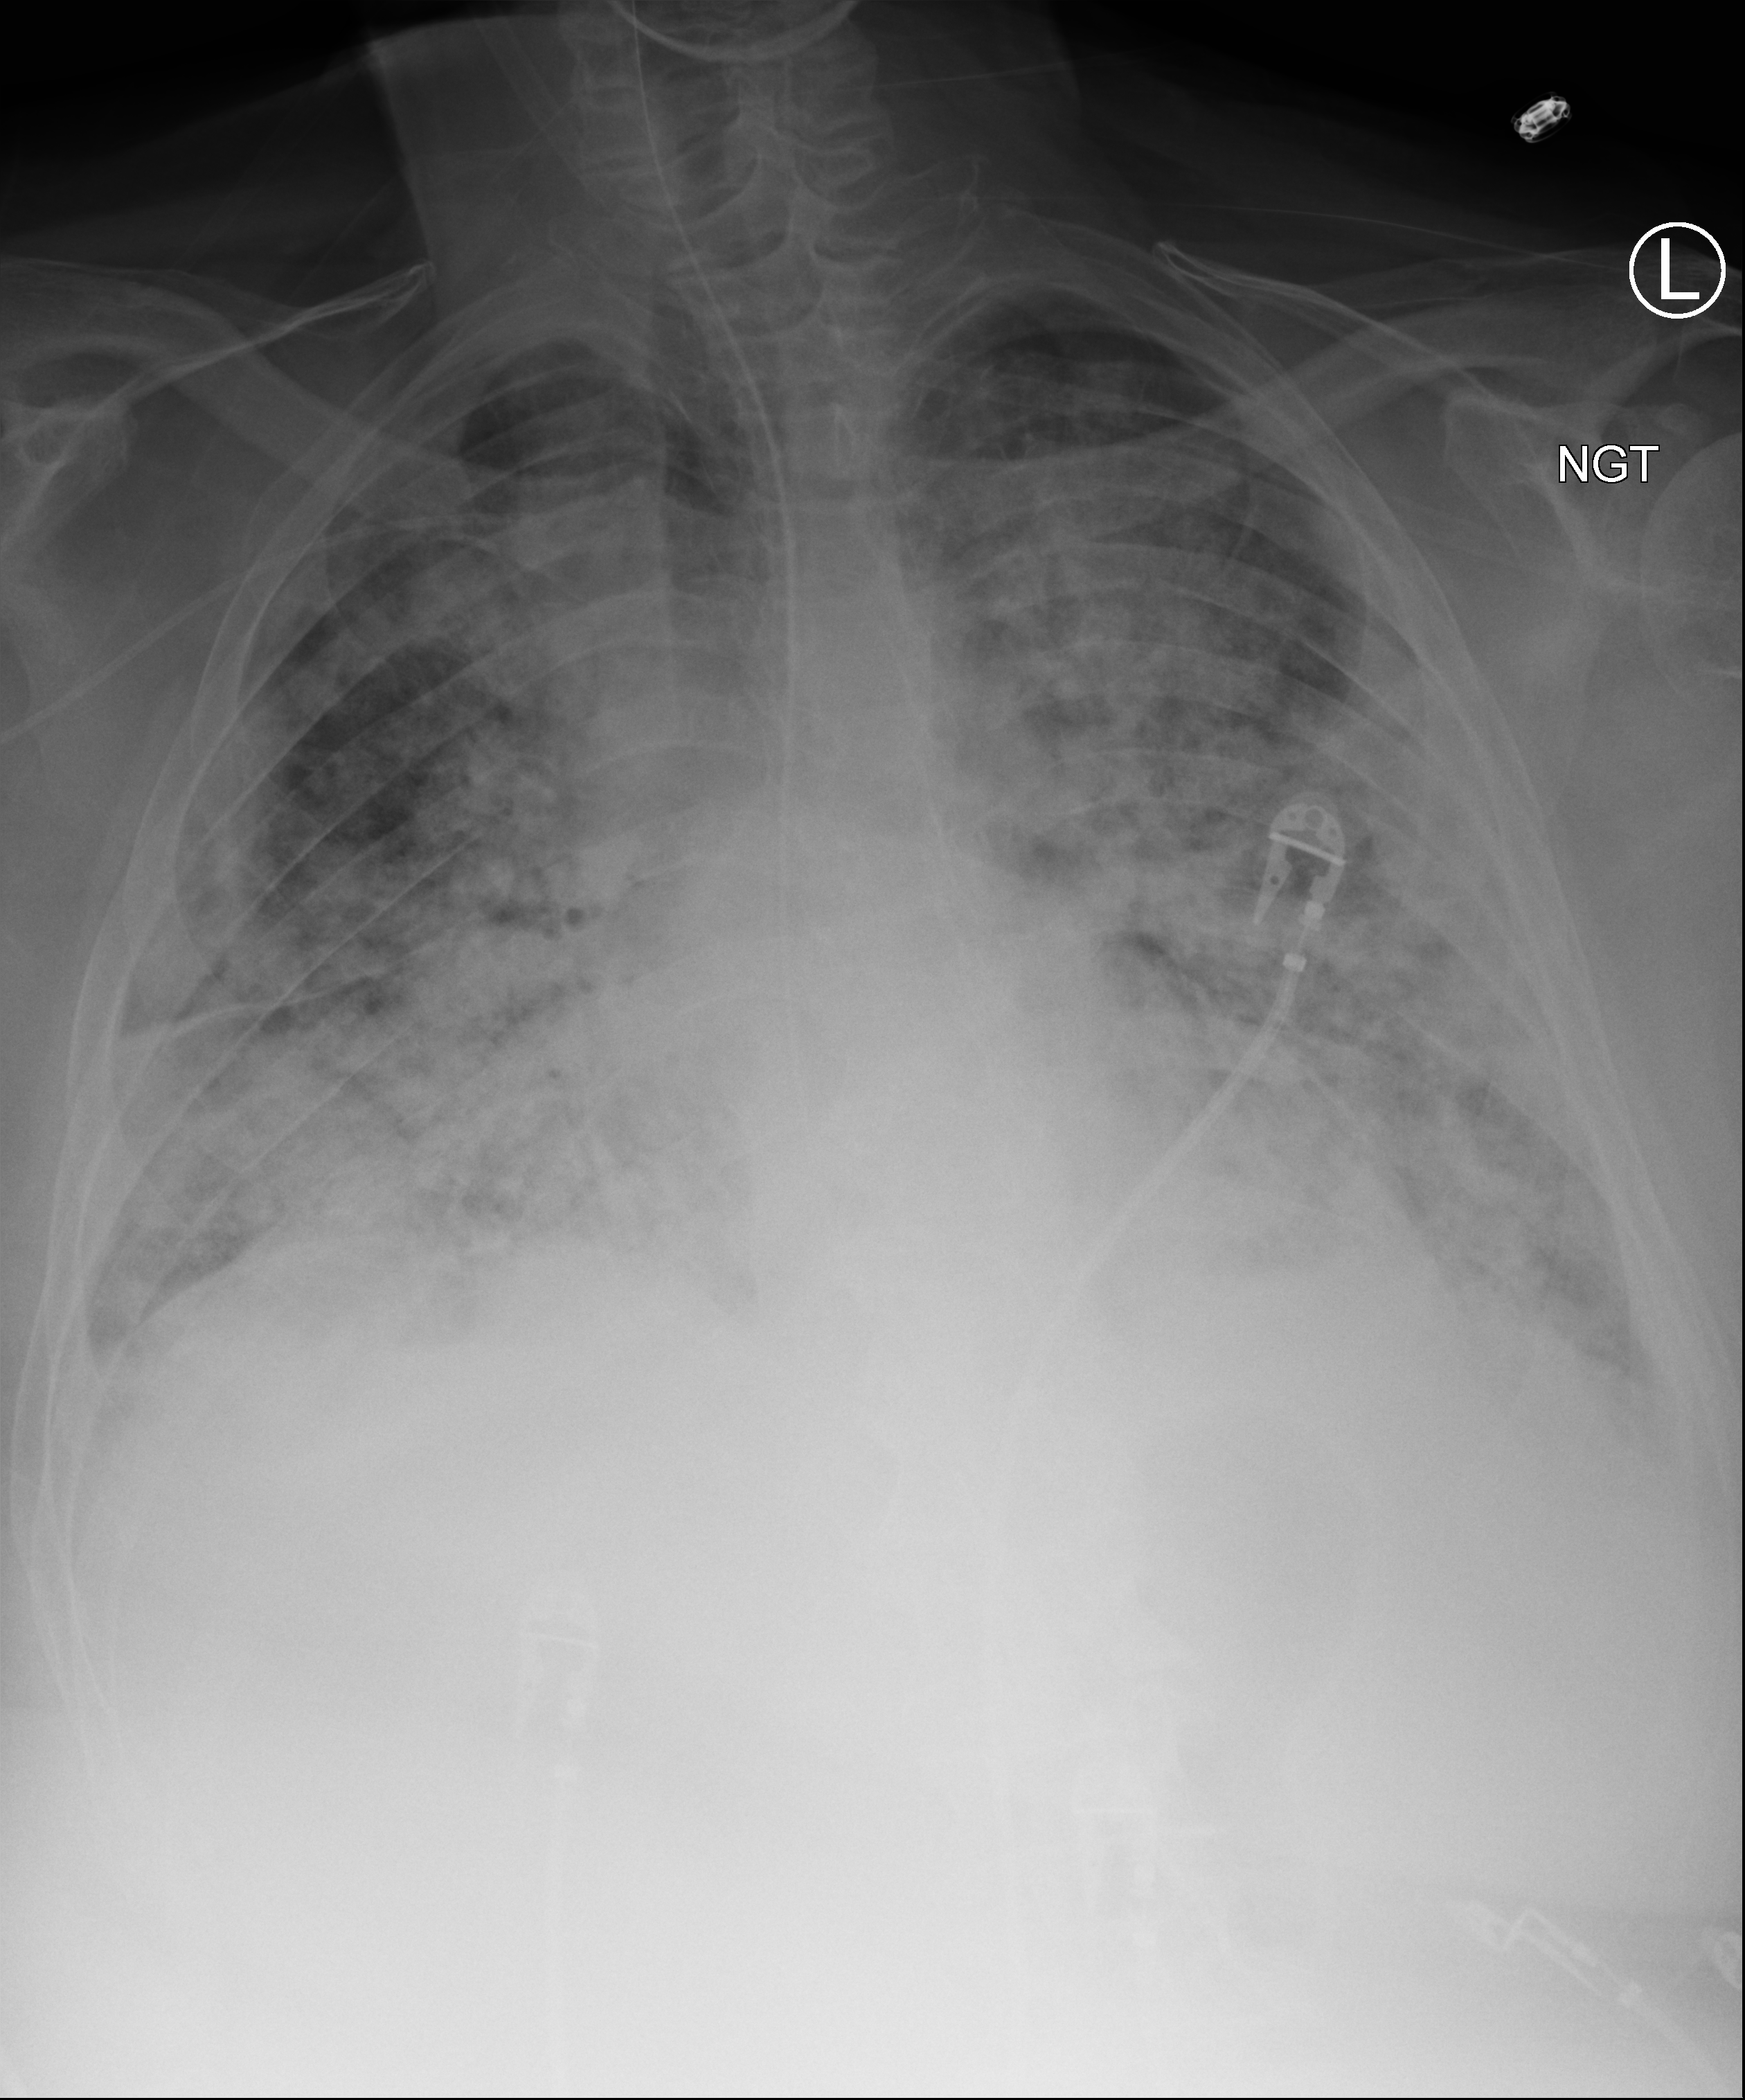
Bedside chest radiograph (computed radiography), anteroposterior (AP) projection. Patient hospitalised with COVID-19; male, aged 60–74 years.
Admission-level facts for this patient (not findings on this image; timing relative to this image not recorded): other chronic lung disease (admission record): no.